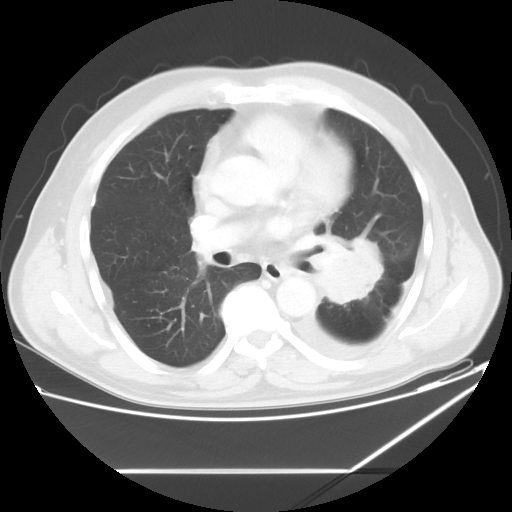
Chest CT, one axial slice. Reconstruction kernel STANDARD. 120 kVp. Lung window (W 1500 / L -600 HU). 5 mm slice thickness. 512 × 512 image matrix, field of view 395 × 395 mm. Male patient, age 62 years. From the clinical record (not read from this slice): clinical TNM (as recorded): T3 N0 M1.
Annotated regions visible in this slice (bounding box drawn by a radiologist):
- lung tumour (recorded histology: adenocarcinoma): bounding box [x1, y1, x2, y2] px = [319, 238, 382, 306]
- lung tumour (recorded histology: adenocarcinoma): [320, 233, 385, 306]